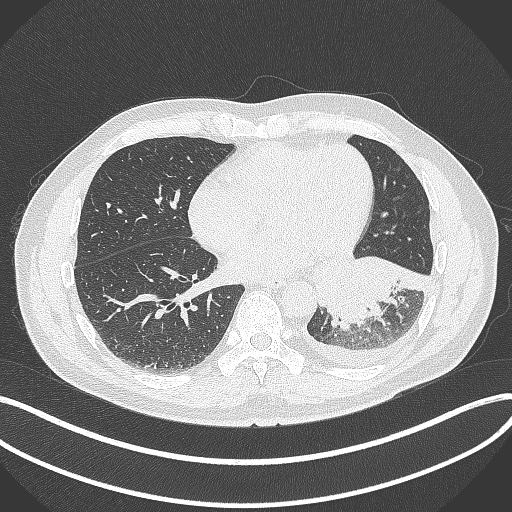
Chest CT, one axial slice; slice 136 of 342 in the series (ordered by position); reconstruction kernel B70f; 120 kVp; lung window (W 1500 / L -600 HU); 1 mm slice thickness; 512 × 512 image matrix. Male patient, age 58 years. Case-level facts recorded for this patient, not image findings: clinical TNM (as recorded): T3 N1 M1b.
Outlined on this slice (bounding box drawn by a radiologist):
- lung tumour (recorded histology: small cell carcinoma): box from (x=310, y=252) to (x=434, y=332) px